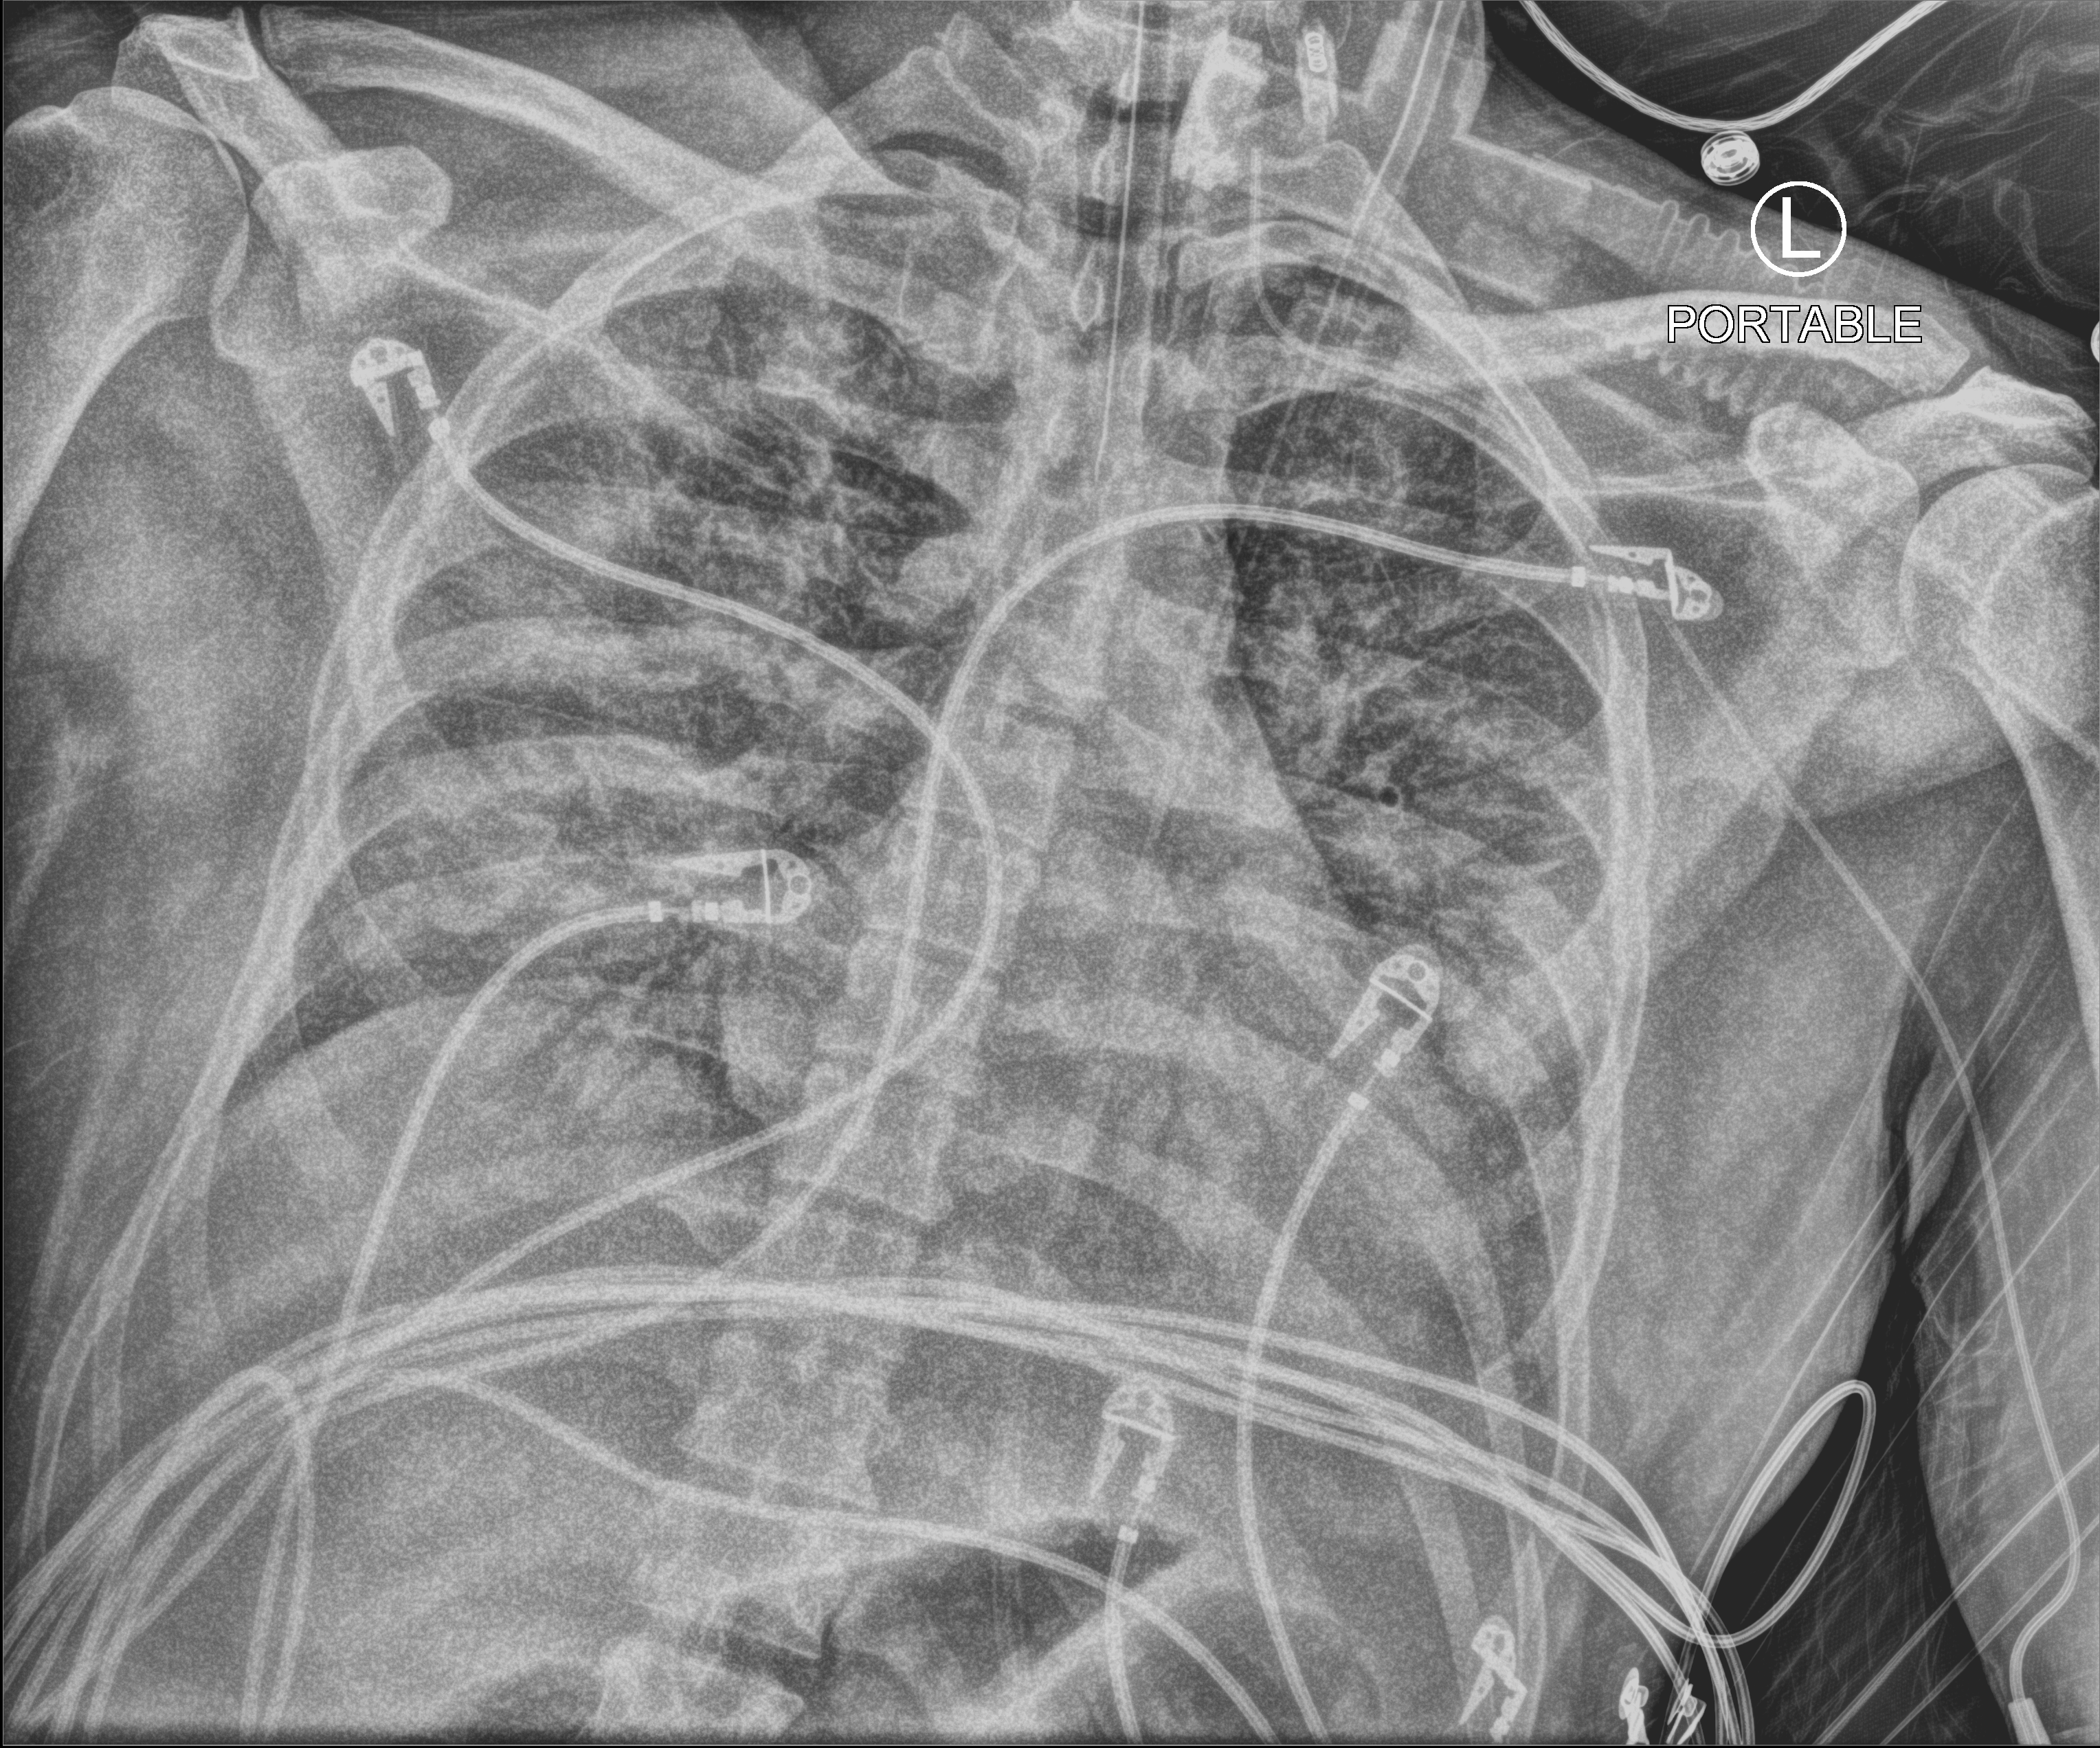
Bedside chest radiograph (computed radiography); anteroposterior (AP) projection. Patient hospitalised with COVID-19; male, aged 18–59 years.
From the hospital-stay record, not from the radiograph (when in the stay this image was taken is not recorded):
- diabetes (admission record): no
- length of hospital stay: 30 days
- other chronic lung disease (admission record): no